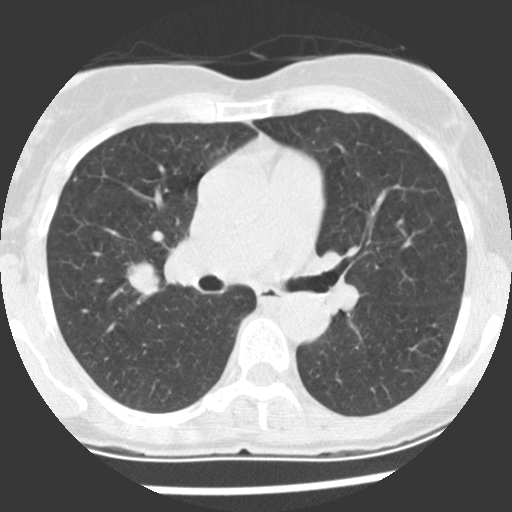
Low-dose screening chest CT, axial slice; baseline annual screen; lung window (W 1500 / L -600 HU); standard (soft-tissue) reconstruction kernel (STANDARD). Female, age 60 years at enrolment. Current smoker at enrolment.
Expert reader's lesion annotation, bounding box [x1, y1, x2, y2] px = [115, 256, 171, 302]. The screening reader recorded 2 non-calcified nodules or masses ≥4 mm on this exam (right upper lobe, right middle lobe); which of them this box marks is not recorded. Official screen result: positive, change unspecified: nodule(s) >= 4 mm or enlarging nodule(s), mass(es), or other non-specific abnormalities suspicious for lung cancer. Participant outcome: lung cancer diagnosed 10 days after this screen — adenocarcinoma, NOS, right upper lobe, stage IIIA (AJCC 6th edition), 20 mm at pathology.